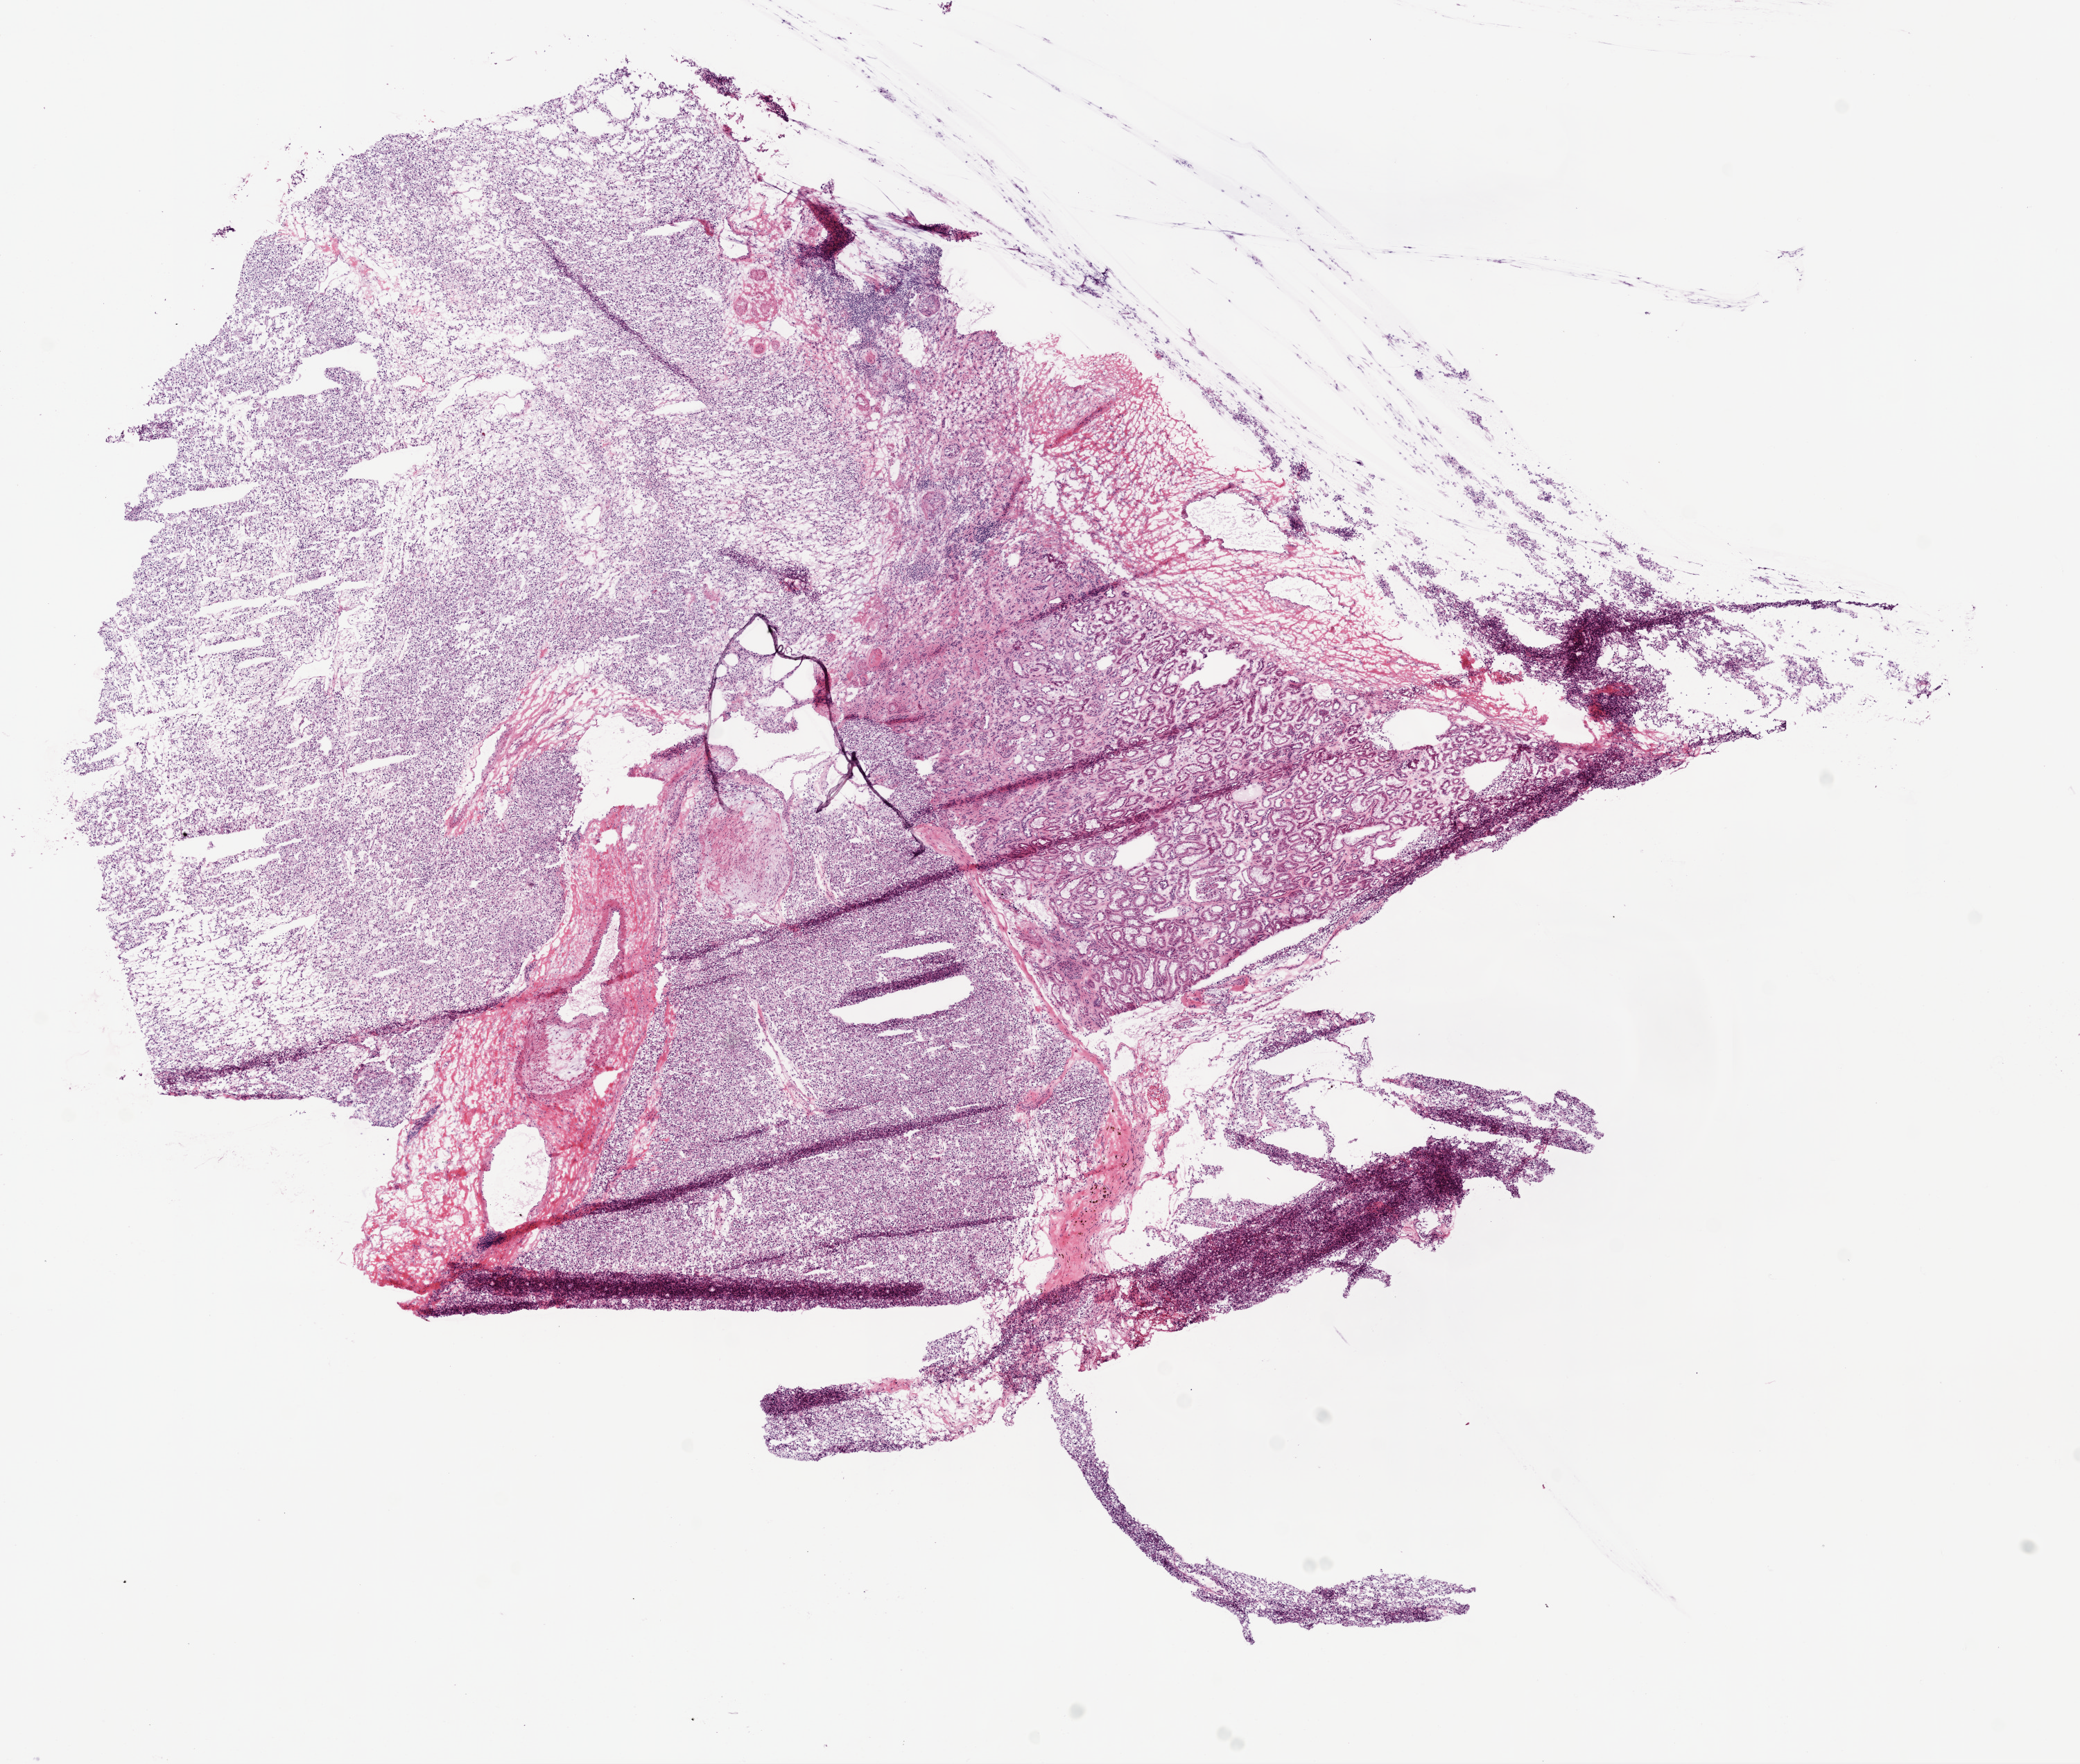
Hematoxylin and eosin (H&E) stained whole-slide image, a low-resolution overview of the entire scanned area, about 12.0 x 10.2 mm (from a 20x scan), frozen section from the bottom of the tissue portion, kidney, primary tumour sample. Female, age 60 years at initial diagnosis. Histologic grade: G2 (moderately differentiated). Composition of this section per pathologist review: tumour cells 65%, tumour nuclei 70%, normal cells 25%, stromal cells 10%, necrosis 0%.
* diagnosis: Clear cell adenocarcinoma, NOS
* laterality: left
* AJCC pathologic stage: I